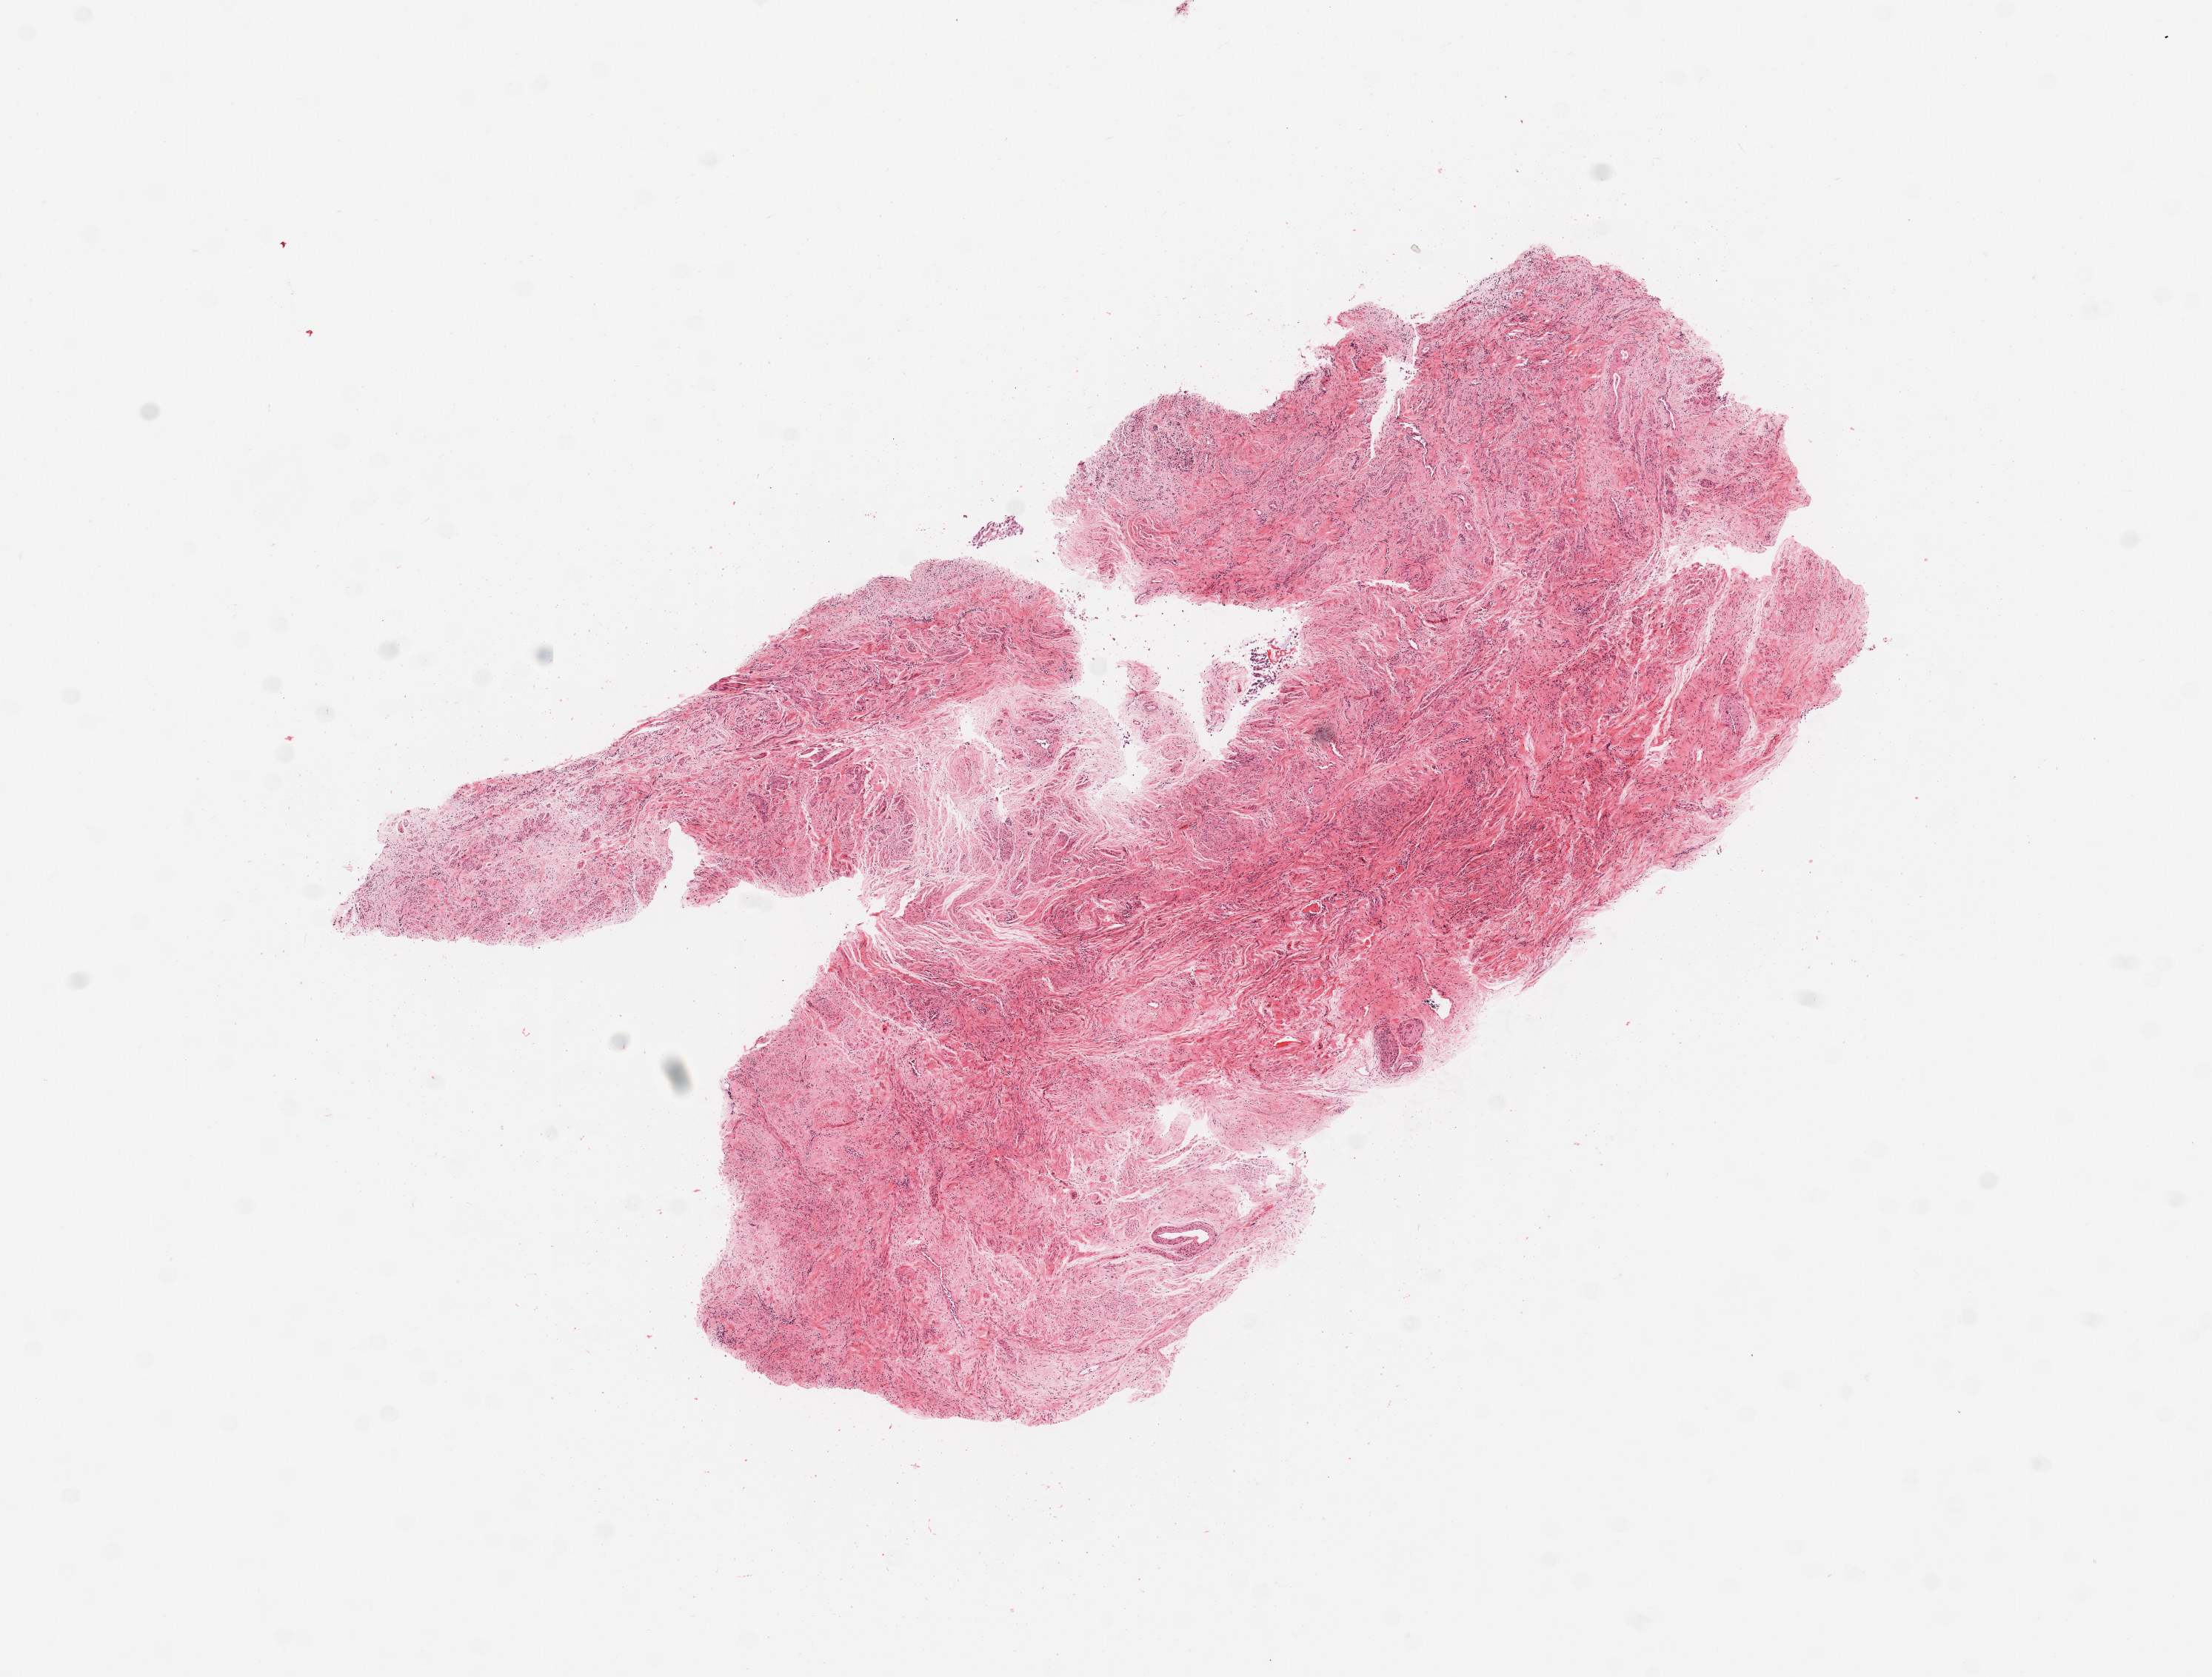
Digitized Hematoxylin and eosin (H&E) stained tissue section (whole slide) — low-resolution overview of the scanned area, about 11.8 x 9.0 mm; uterus, normal (non-tumour) tissue. Patient: female, age 81 years.
- this section: normal (non-tumour) tissue from the same patient
- patient diagnosis: Endometrioid adenocarcinoma, NOS